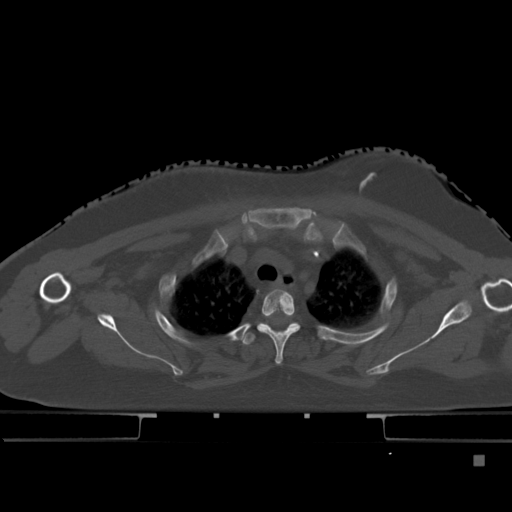
CT including the spine, one axial slice. Slice 355 of 495 in the series (ordered by position). Bone window (W 1800 / L 400 HU). 1.5 mm slice thickness. 512 × 512 image matrix. Female patient, age 33 years. Case-level facts recorded for this patient, not image findings: primary cancer: breast.
Annotated regions visible in this slice (semi-automatically segmented with operator editing):
- T2 vertebra: box from (x=257, y=289) to (x=300, y=364) px
- T3 vertebra: (x=242, y=322)–(x=300, y=345)